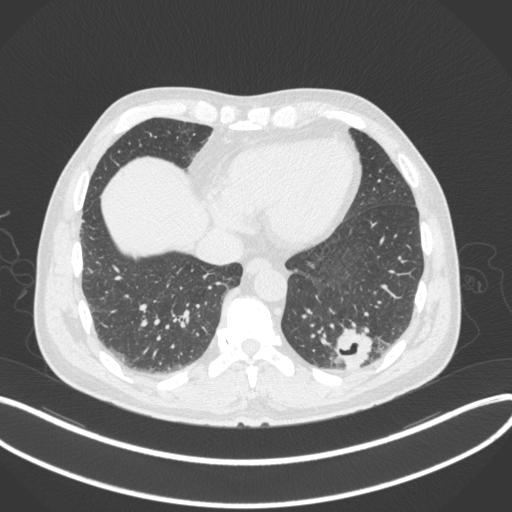
Chest CT, one axial slice. Position 76 of 313 along the scan axis. 120 kVp. Lung window (W 1500 / L -600 HU). 1 mm slice thickness. 512 × 512 image matrix, field of view 400 × 400 mm. Male patient, age 54 years. Case-level facts recorded for this patient, not image findings: clinical TNM (as recorded): T1c N0 M1; histopathological grade: G3.
Outlined on this slice (bounding box drawn by a radiologist):
- lung tumour (recorded histology: adenocarcinoma): bounding box (x1, y1, x2, y2) in pixels: (333, 323, 375, 368)